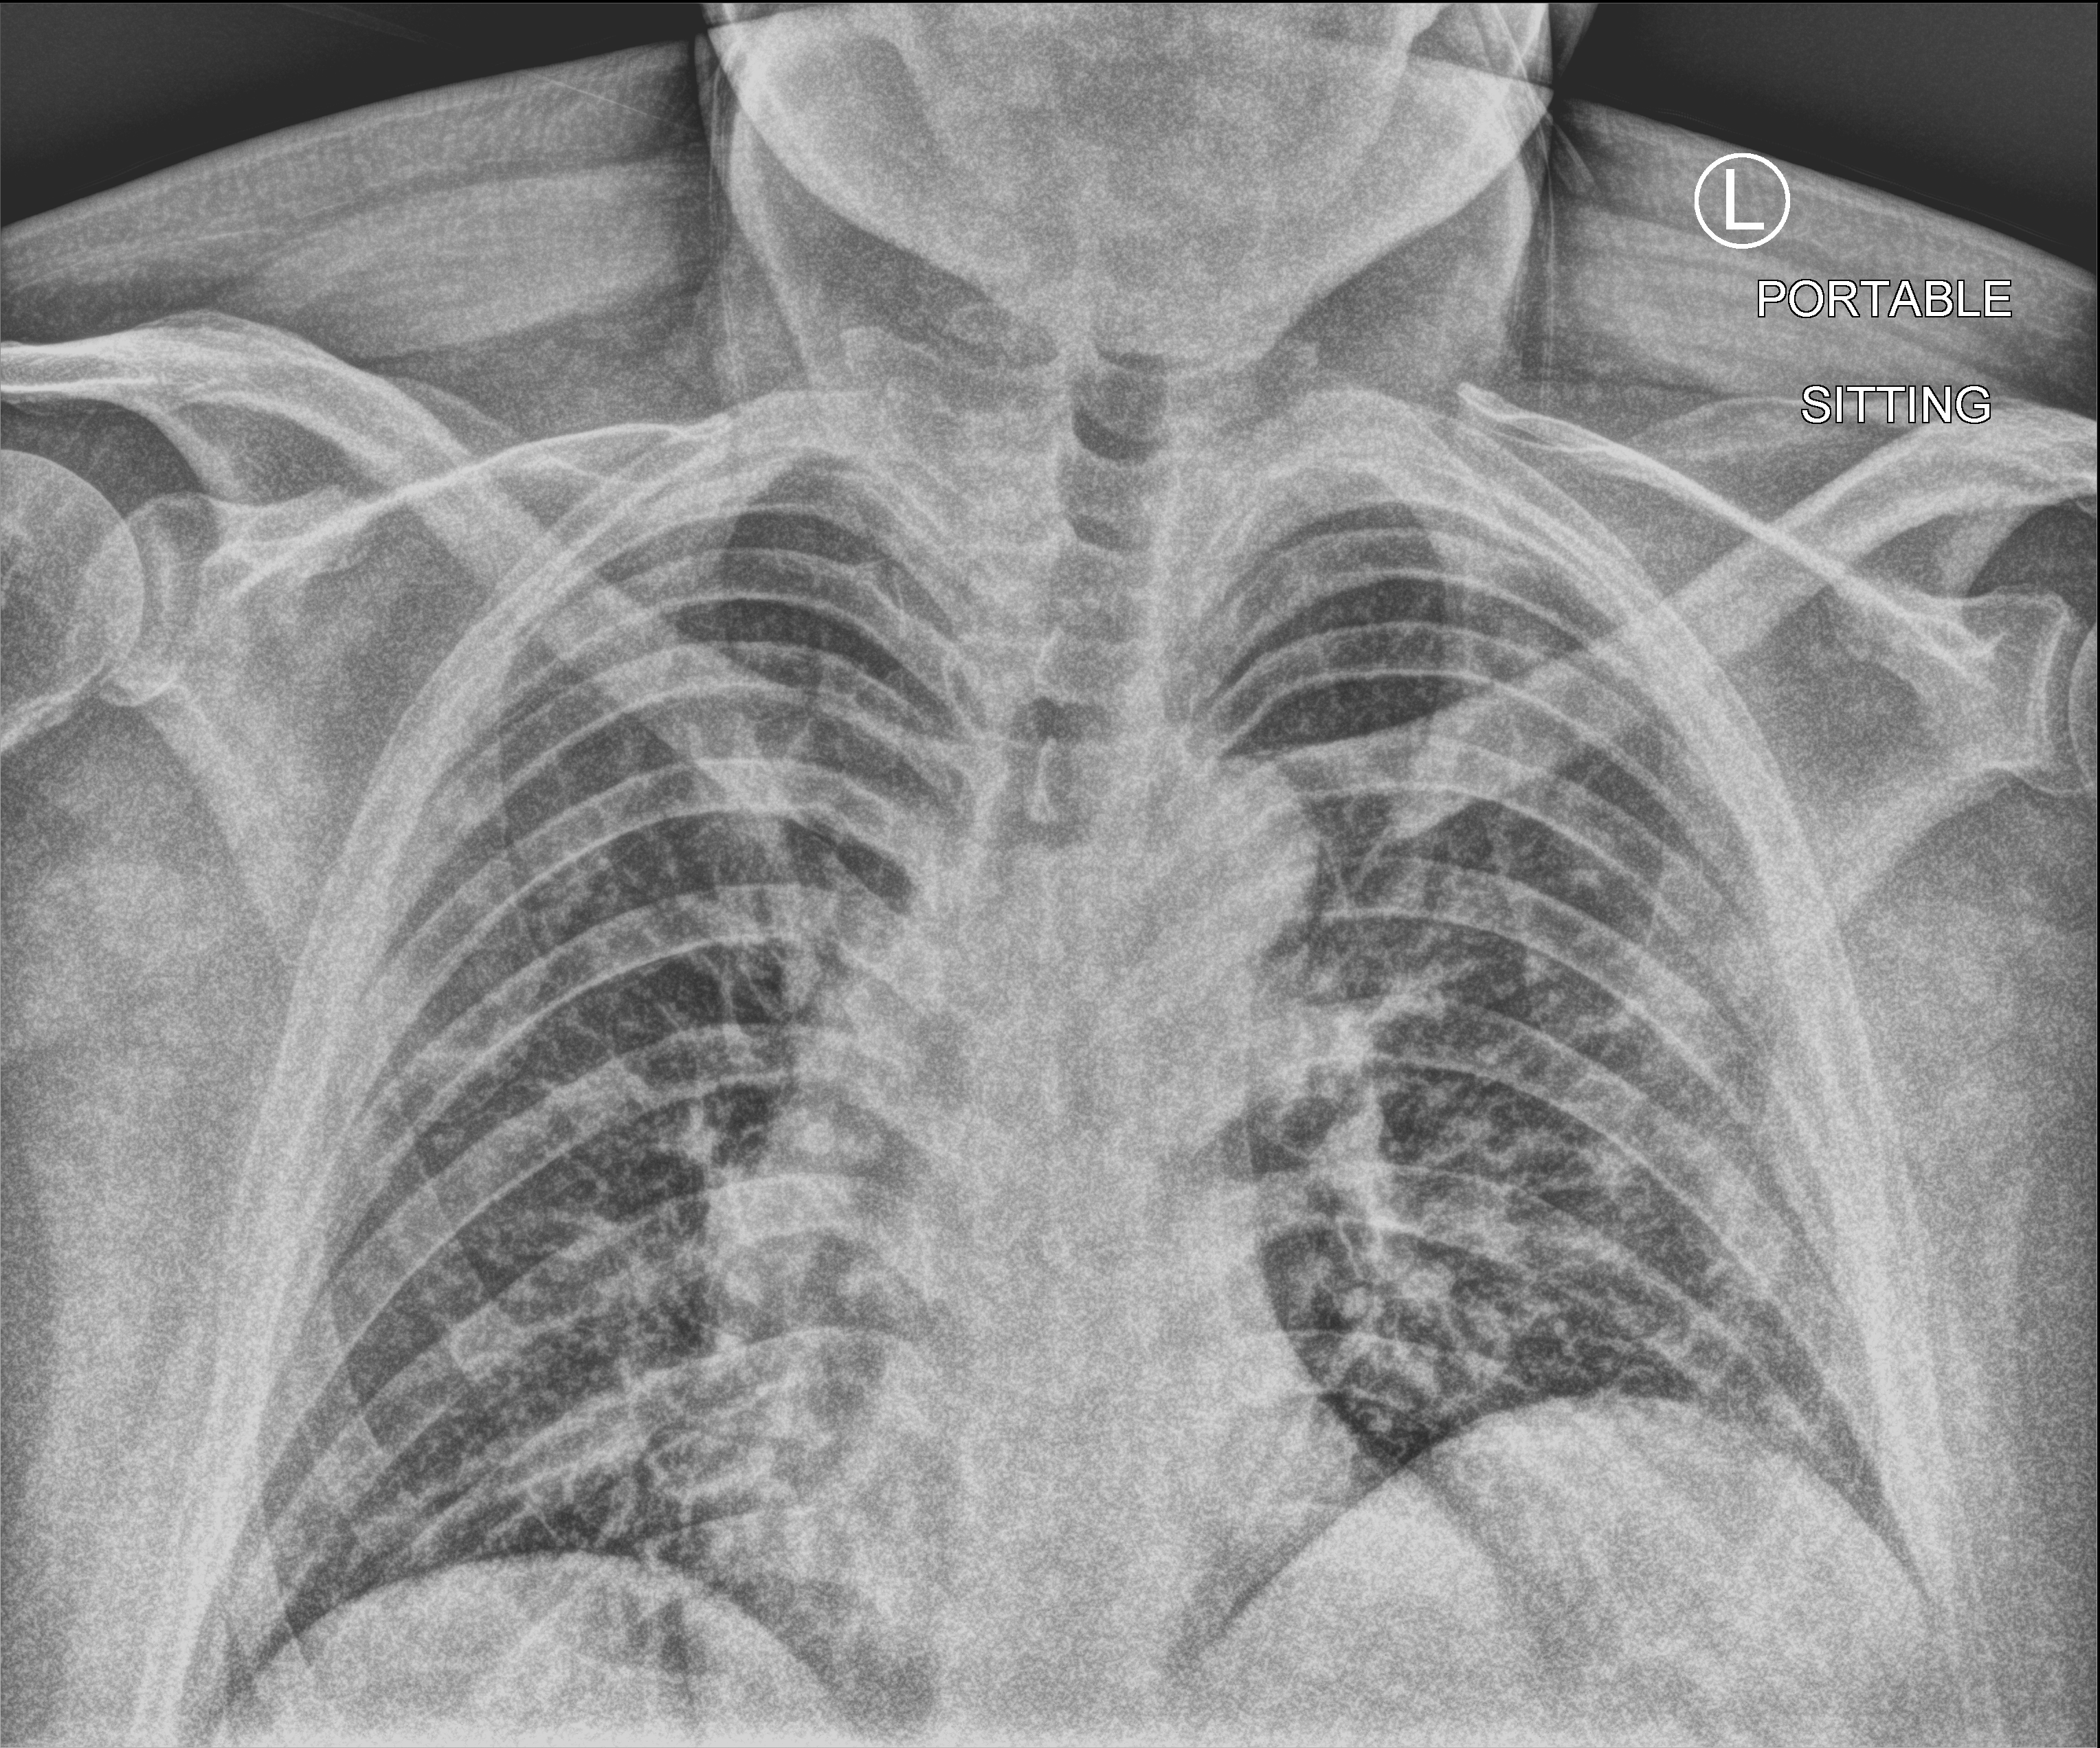
Chest X-ray (portable), anteroposterior (AP) projection. Male patient hospitalised with COVID-19, age 18–59 years.
From the hospital-stay record, not from the radiograph (when in the stay this image was taken is not recorded):
- smoking status (admission record): never